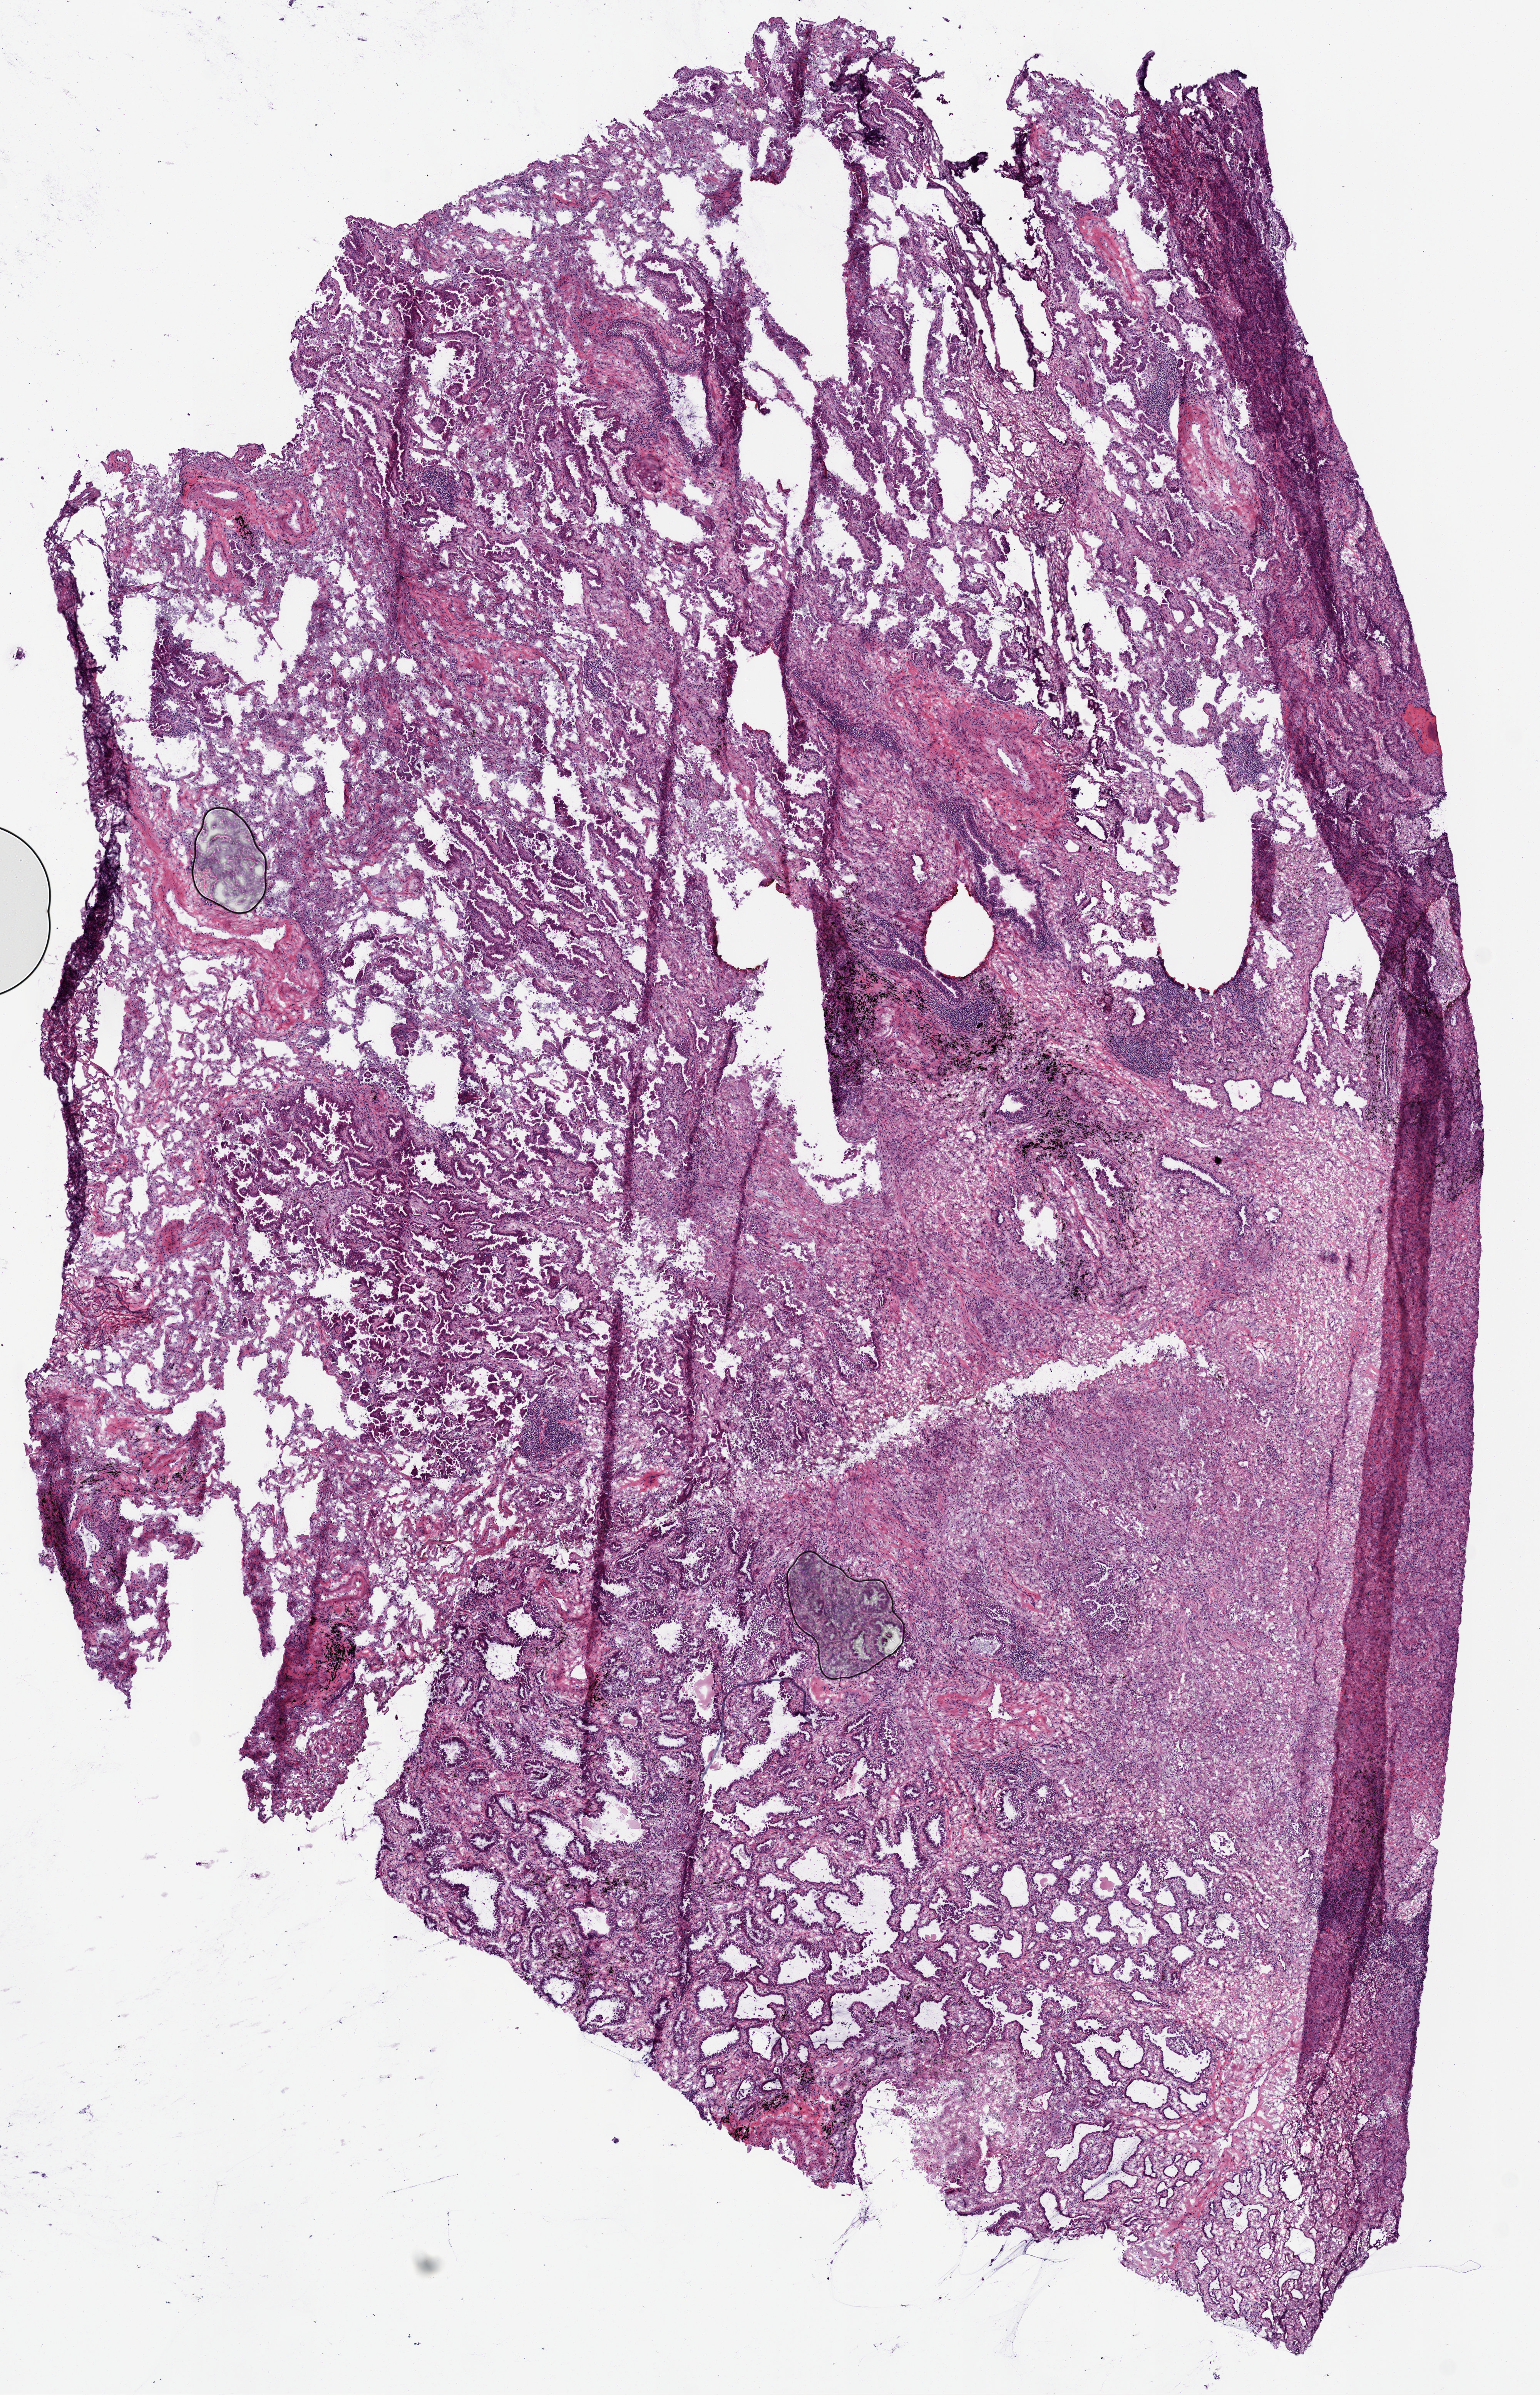
H&E-stained whole-slide image — low-resolution overview of the scanned area, about 8.0 x 12.5 mm; frozen section from the top of the tissue portion; primary tumour sample from the lung. Female, age 72 years at initial diagnosis. Composition of this section per pathologist review: tumour cells 95%, tumour nuclei 80%, normal cells 5%, stromal cells 0%, necrosis 0%. Infiltration values recorded for this section: lymphocyte infiltration 5%, monocyte infiltration 5%, neutrophil infiltration 0%.
Diagnosis: Acinar cell carcinoma. TNM: T1b N0 MX. AJCC pathologic stage: IA (7th edition). Laterality: left.